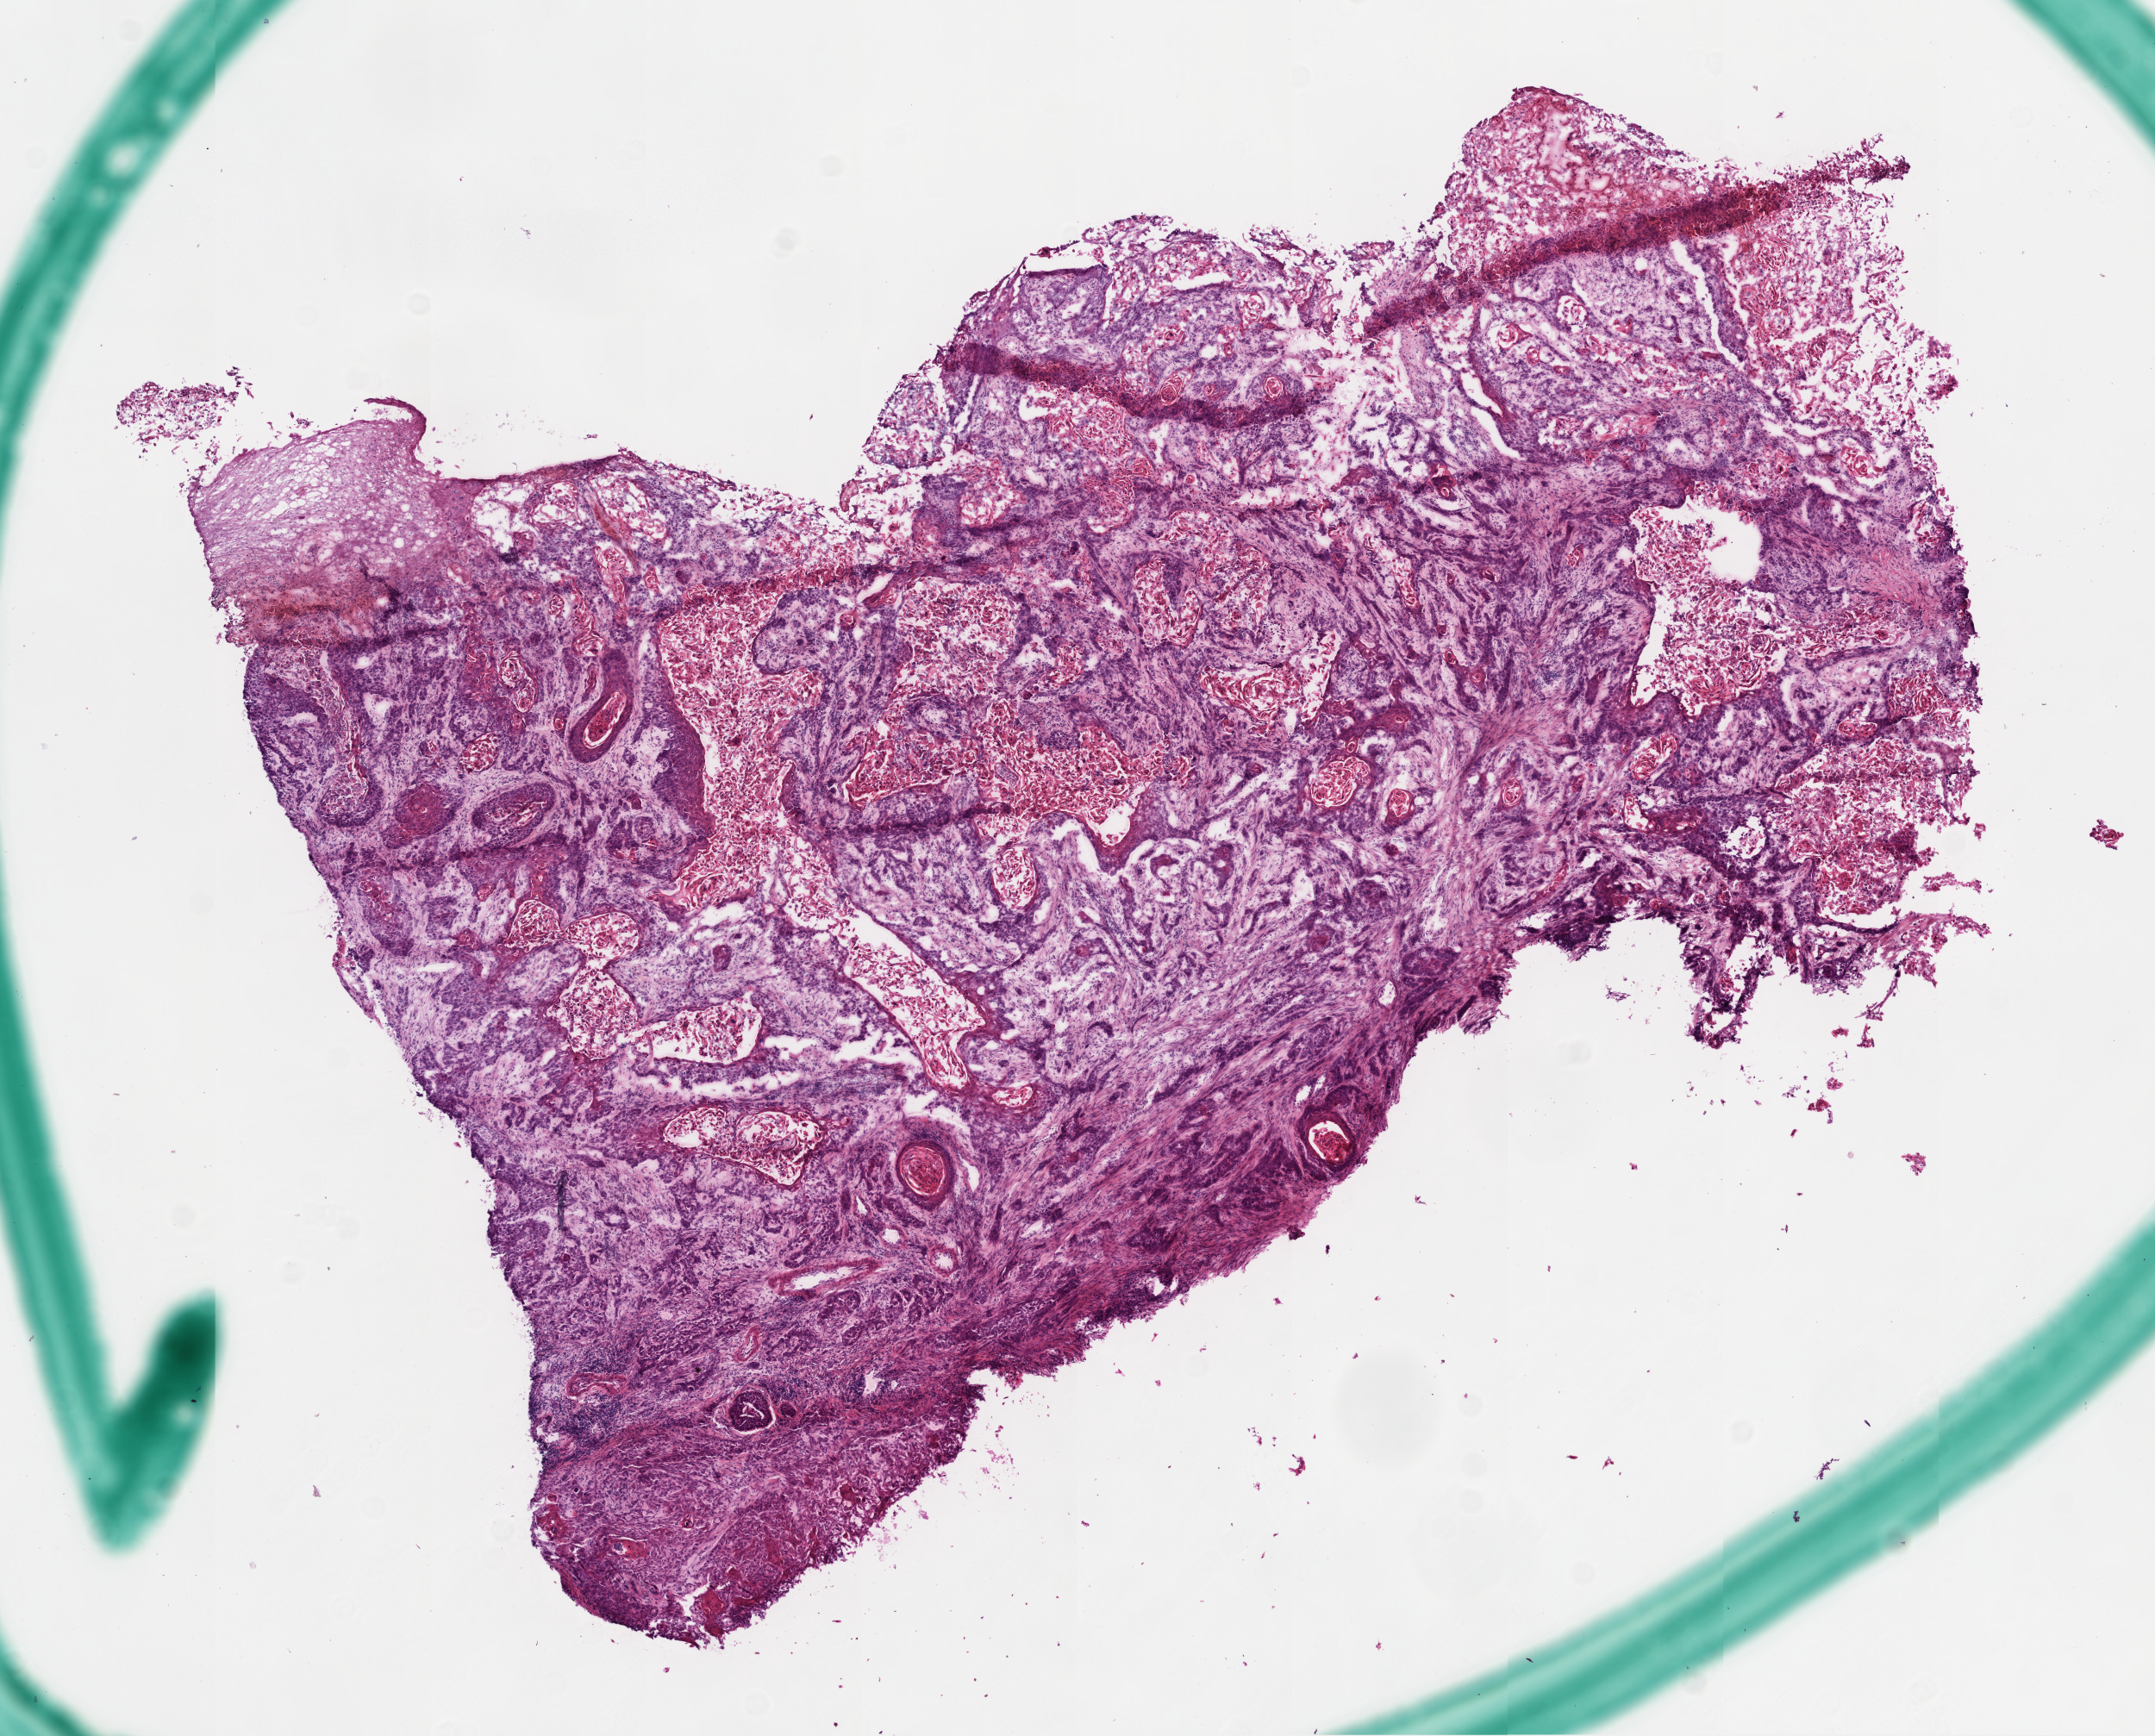
Hematoxylin and eosin (H&E) stained whole-slide image — whole scanned area (about 10.0 x 8.1 mm, from a 20x scan) shown as a low-resolution overview. Frozen section from the top of the tissue portion. Sample: primary tumour, head and neck. Male, age 68 years at initial diagnosis. Histologic grade: G3 (poorly differentiated). Slide review estimates, as recorded: tumour cells 73%, tumour nuclei 80%, normal cells 6%, stromal cells 0%, necrosis 21%. Inflammatory infiltration, as recorded: lymphocyte infiltration 10%.
- histologic diagnosis: Squamous cell carcinoma, NOS (larynx, NOS)
- AJCC pathologic stage: IVA (7th edition)
- TNM: T4a N2c M0